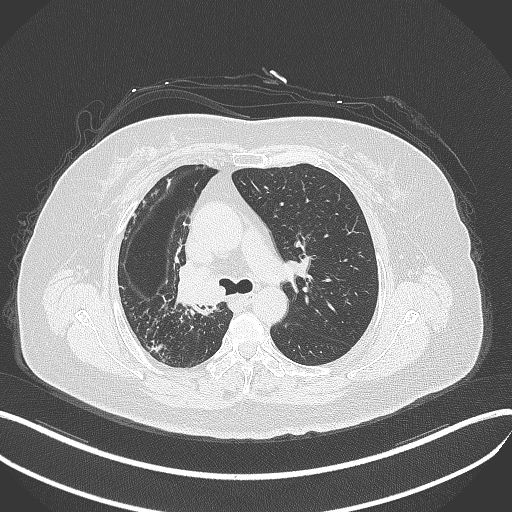
Chest CT, one axial slice. Position 235 of 376 along the scan axis. Reconstruction kernel B70f. 120 kVp. Lung window (W 1500 / L -600 HU). 512 × 512 image matrix. Female patient, age 60 years. From the clinical record (not read from this slice): clinical TNM (as recorded): T1c N0 M0; histopathological grade: G1-G2.
Outlined on this slice (bounding box drawn by a radiologist):
- lung tumour (recorded histology: squamous cell carcinoma): bounding box <169,259,230,311> (left, top, right, bottom; pixels)